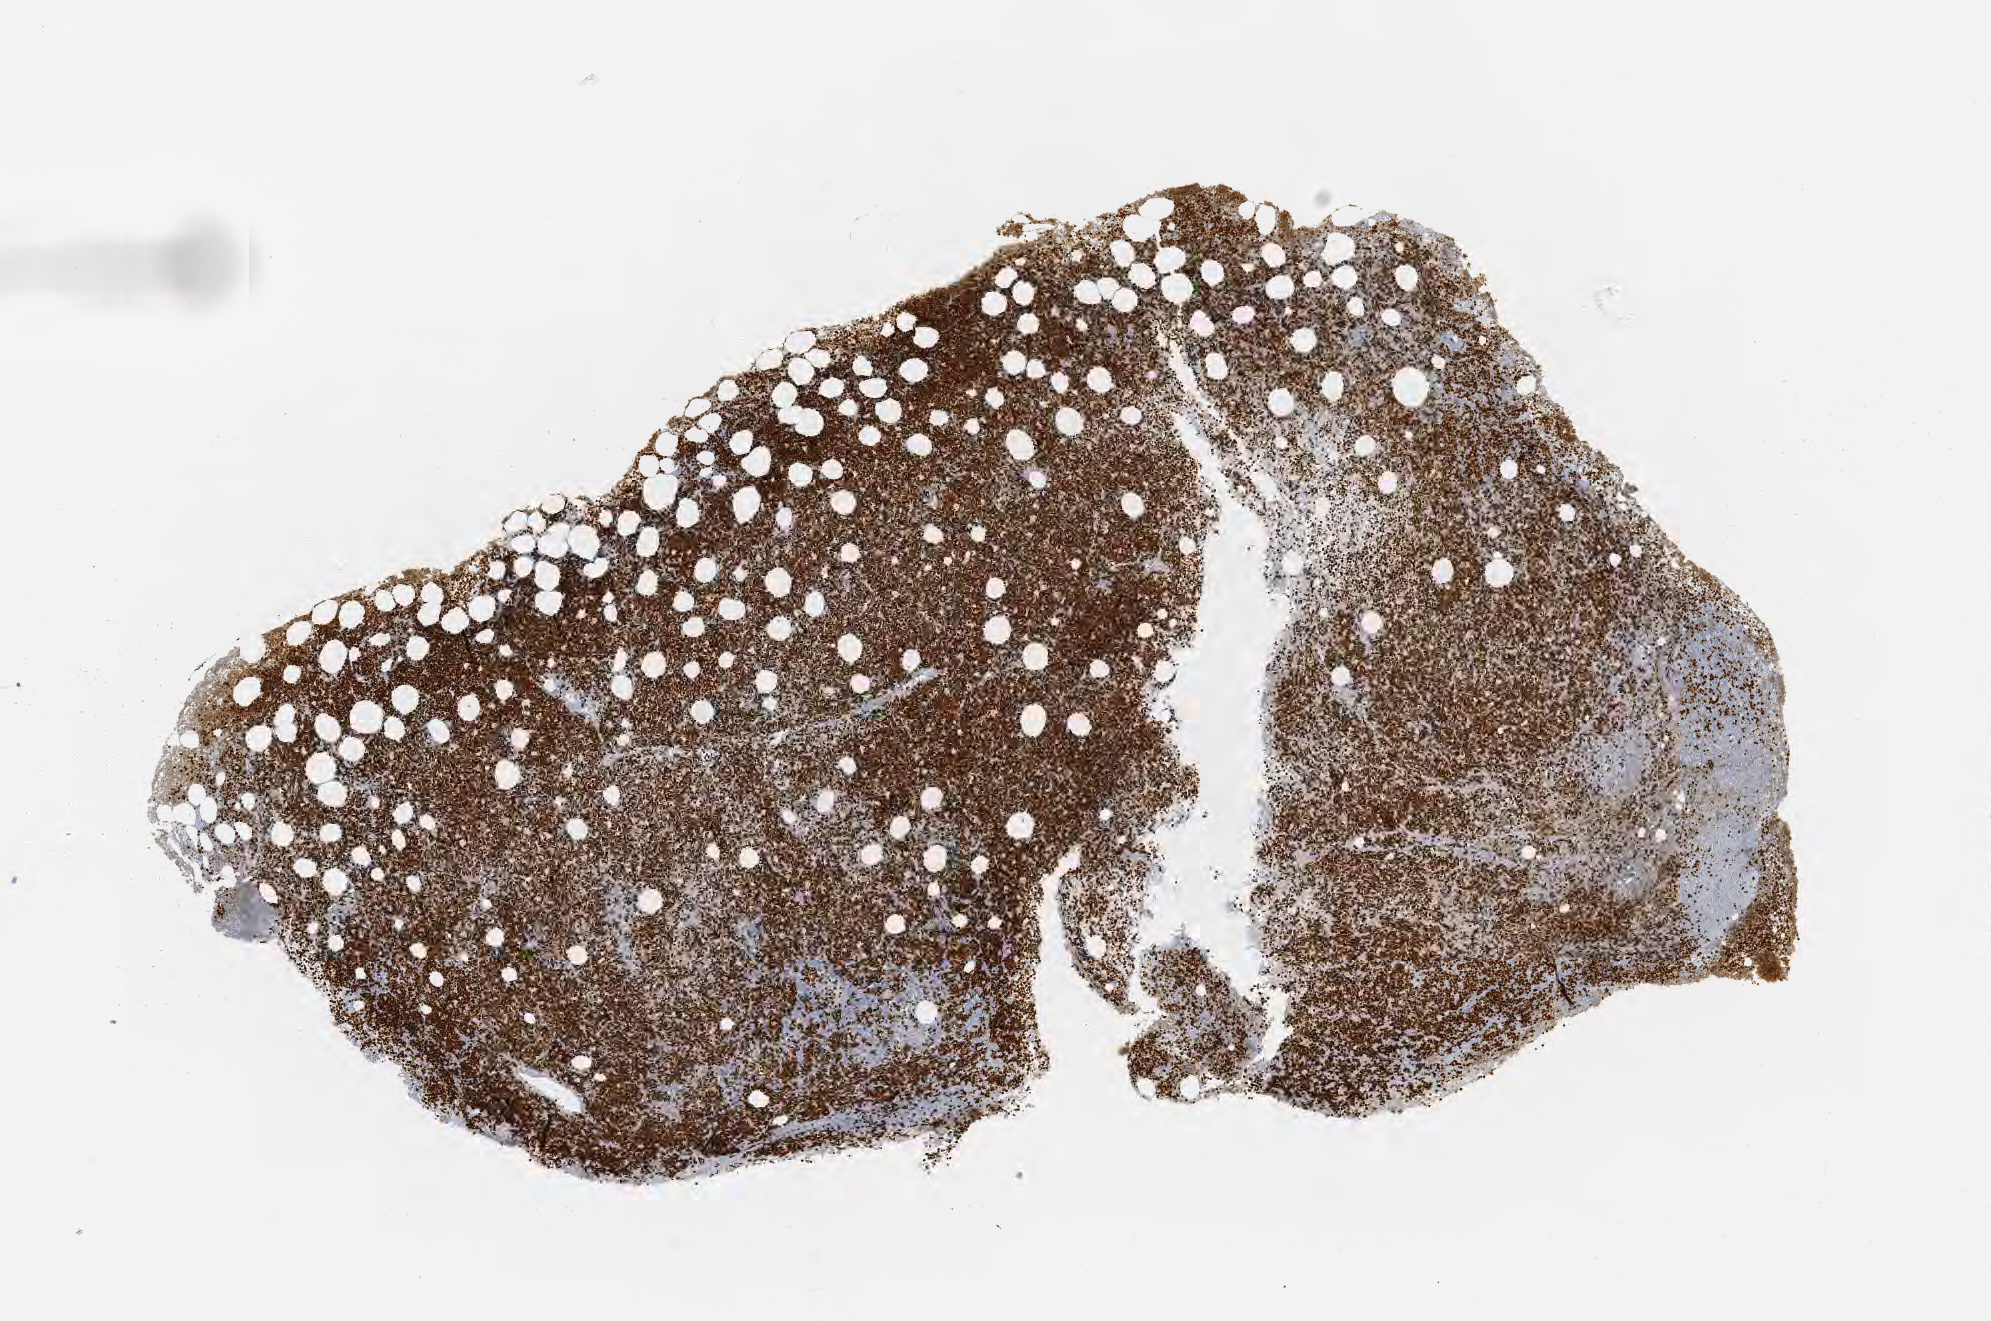
Whole-slide image, immunohistochemical stain for Ki-67, a low-resolution overview of the entire scanned area, about 8.1 x 5.3 mm; tumor tissue; site: bone marrow. Patient: male, aged 70.
Diagnosis: Neoplasm, uncertain whether benign or malignant.